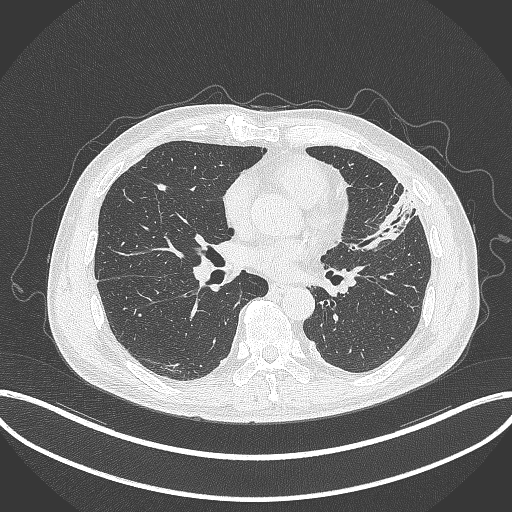
Chest CT, one axial slice. Position 155 of 382 along the scan axis. 120 kVp. Lung window (W 1500 / L -600 HU). 1 mm slice thickness. 512 × 512 image matrix, field of view 415 × 415 mm. Patient: male, 64 years. From the clinical record (not read from this slice): clinical TNM (as recorded): T4 N1 M0.
Annotated regions visible in this slice (bounding box drawn by a radiologist):
- lung tumour (recorded histology: adenocarcinoma): bounding box <359,186,417,247> (left, top, right, bottom; pixels)